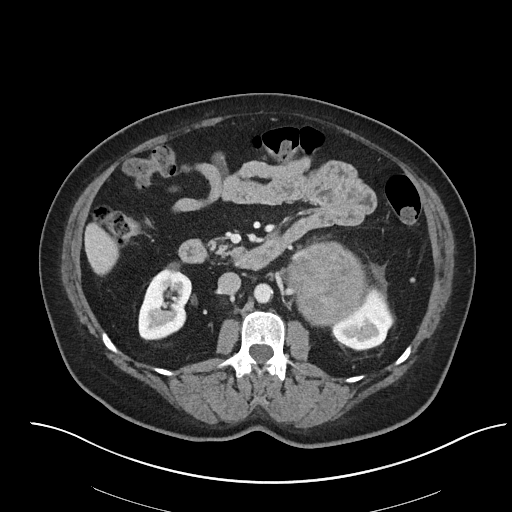
Contrast-enhanced abdominal CT, one axial slice; position 32 of 92 along the scan axis; reconstruction kernel I40f/2; 120 kVp; intravenous contrast given; soft-tissue window (W 400 / L 40 HU); 3 mm slice thickness; 512 × 512 image matrix, field of view 440 × 440 mm. Patient: female, 53 years. Case-level facts recorded for this patient, not image findings: diagnosis: adrenocortical carcinoma; tumour side: left adrenal; tumour size at pathology: 9 cm; Ki-67 index: 28 %.
Structures marked on this image (semi-automatically segmented with operator editing):
- mass: bounding box [x1, y1, x2, y2] px = [288, 244, 363, 324]